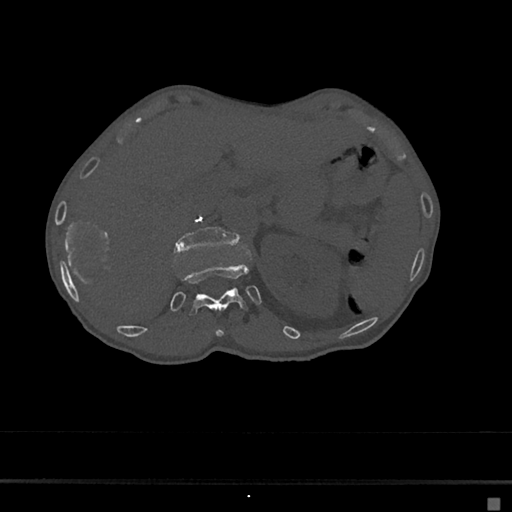
CT including the spine, one axial slice; position 118 of 797 along the scan axis; bone window (W 1800 / L 400 HU); 0.5 mm slice thickness; 512 × 512 image matrix. Female patient, age 68 years. Case-level facts recorded for this patient, not image findings: primary cancer: renal.
Outlined on this slice (semi-automatically segmented with operator editing):
- L1 vertebra: bounding box [x1, y1, x2, y2] px = [173, 226, 239, 254]
- T11 vertebra: [215, 328, 224, 337]
- T12 vertebra: [175, 262, 248, 317]